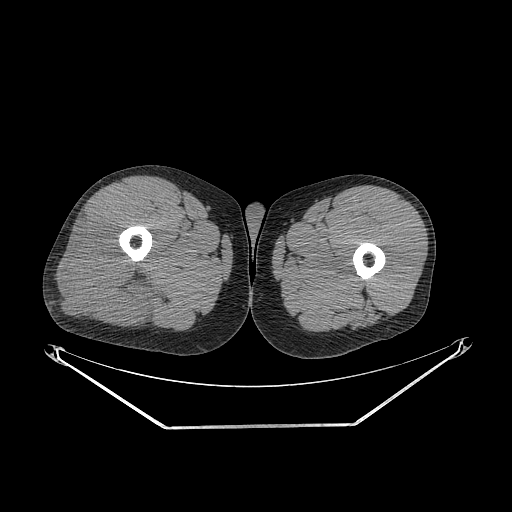
CT of an extremity soft-tissue mass (from a PET/CT study), one axial slice. Position 254 of 267 along the scan axis. 140 kVp. Soft-tissue window (W 400 / L 40 HU). 3.75 mm slice thickness. 512 × 512 image matrix. Male patient. From the clinical record (not read from this slice): histological type: poorly differentiated synovial sarcoma; grade: high; site of the primary tumour: right buttock.
Annotated regions visible in this slice (expert contour drawn on MRI and transferred to this co-registered scan by the dataset authors):
- gross tumour volume including surrounding oedema: bounding box (x1, y1, x2, y2) in pixels: (59, 219, 154, 323)
- gross tumour volume (mass): (59, 219, 154, 323)